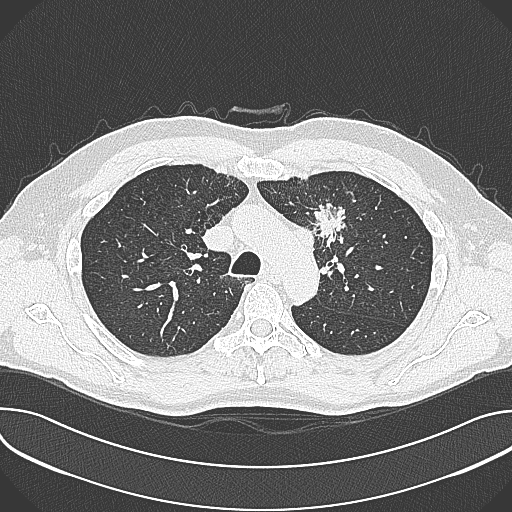
Chest CT (low-dose screening protocol), one axial image, first (baseline) screen, lung window (W 1500 / L -600 HU), 1 mm slice thickness, lung (sharp) reconstruction kernel (B80f), slice 95 of 361 in the series, 512 × 512 image matrix, field of view 380 × 380 mm. Male, age 59 years at enrolment. Current smoker at enrolment.
Lesion marked by an expert reader, bounding box [x1, y1, x2, y2] px = [302, 199, 360, 257]. The screening reader recorded 2 non-calcified nodules or masses ≥4 mm on this exam; which of them this box marks is not recorded.